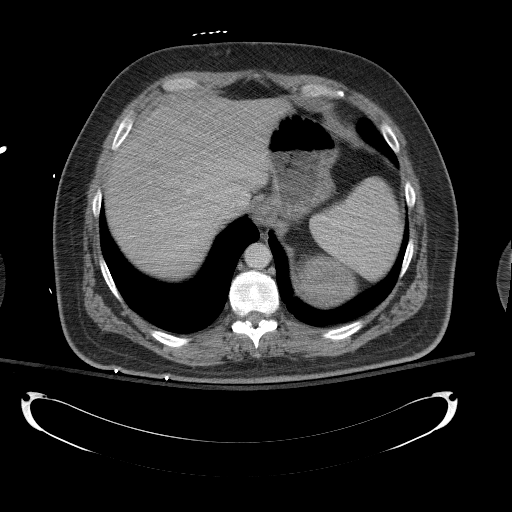
Contrast-enhanced abdominal CT, one axial slice; slice 99 of 154 in the series (ordered by position); intravenous contrast given; soft-tissue window (W 400 / L 40 HU); 5 mm slice thickness; 512 × 512 image matrix. Patient: male, 43 years. From the clinical record (not read from this slice): diagnosis: adrenocortical carcinoma; tumour side: left adrenal; tumour size at pathology: 9.8 cm; Ki-67 index: 30 %; stage (as recorded): 2.
Outlined on this slice (semi-automatic segmentation, software-assisted and operator-edited):
- mass: box from (x=301, y=254) to (x=356, y=305) px